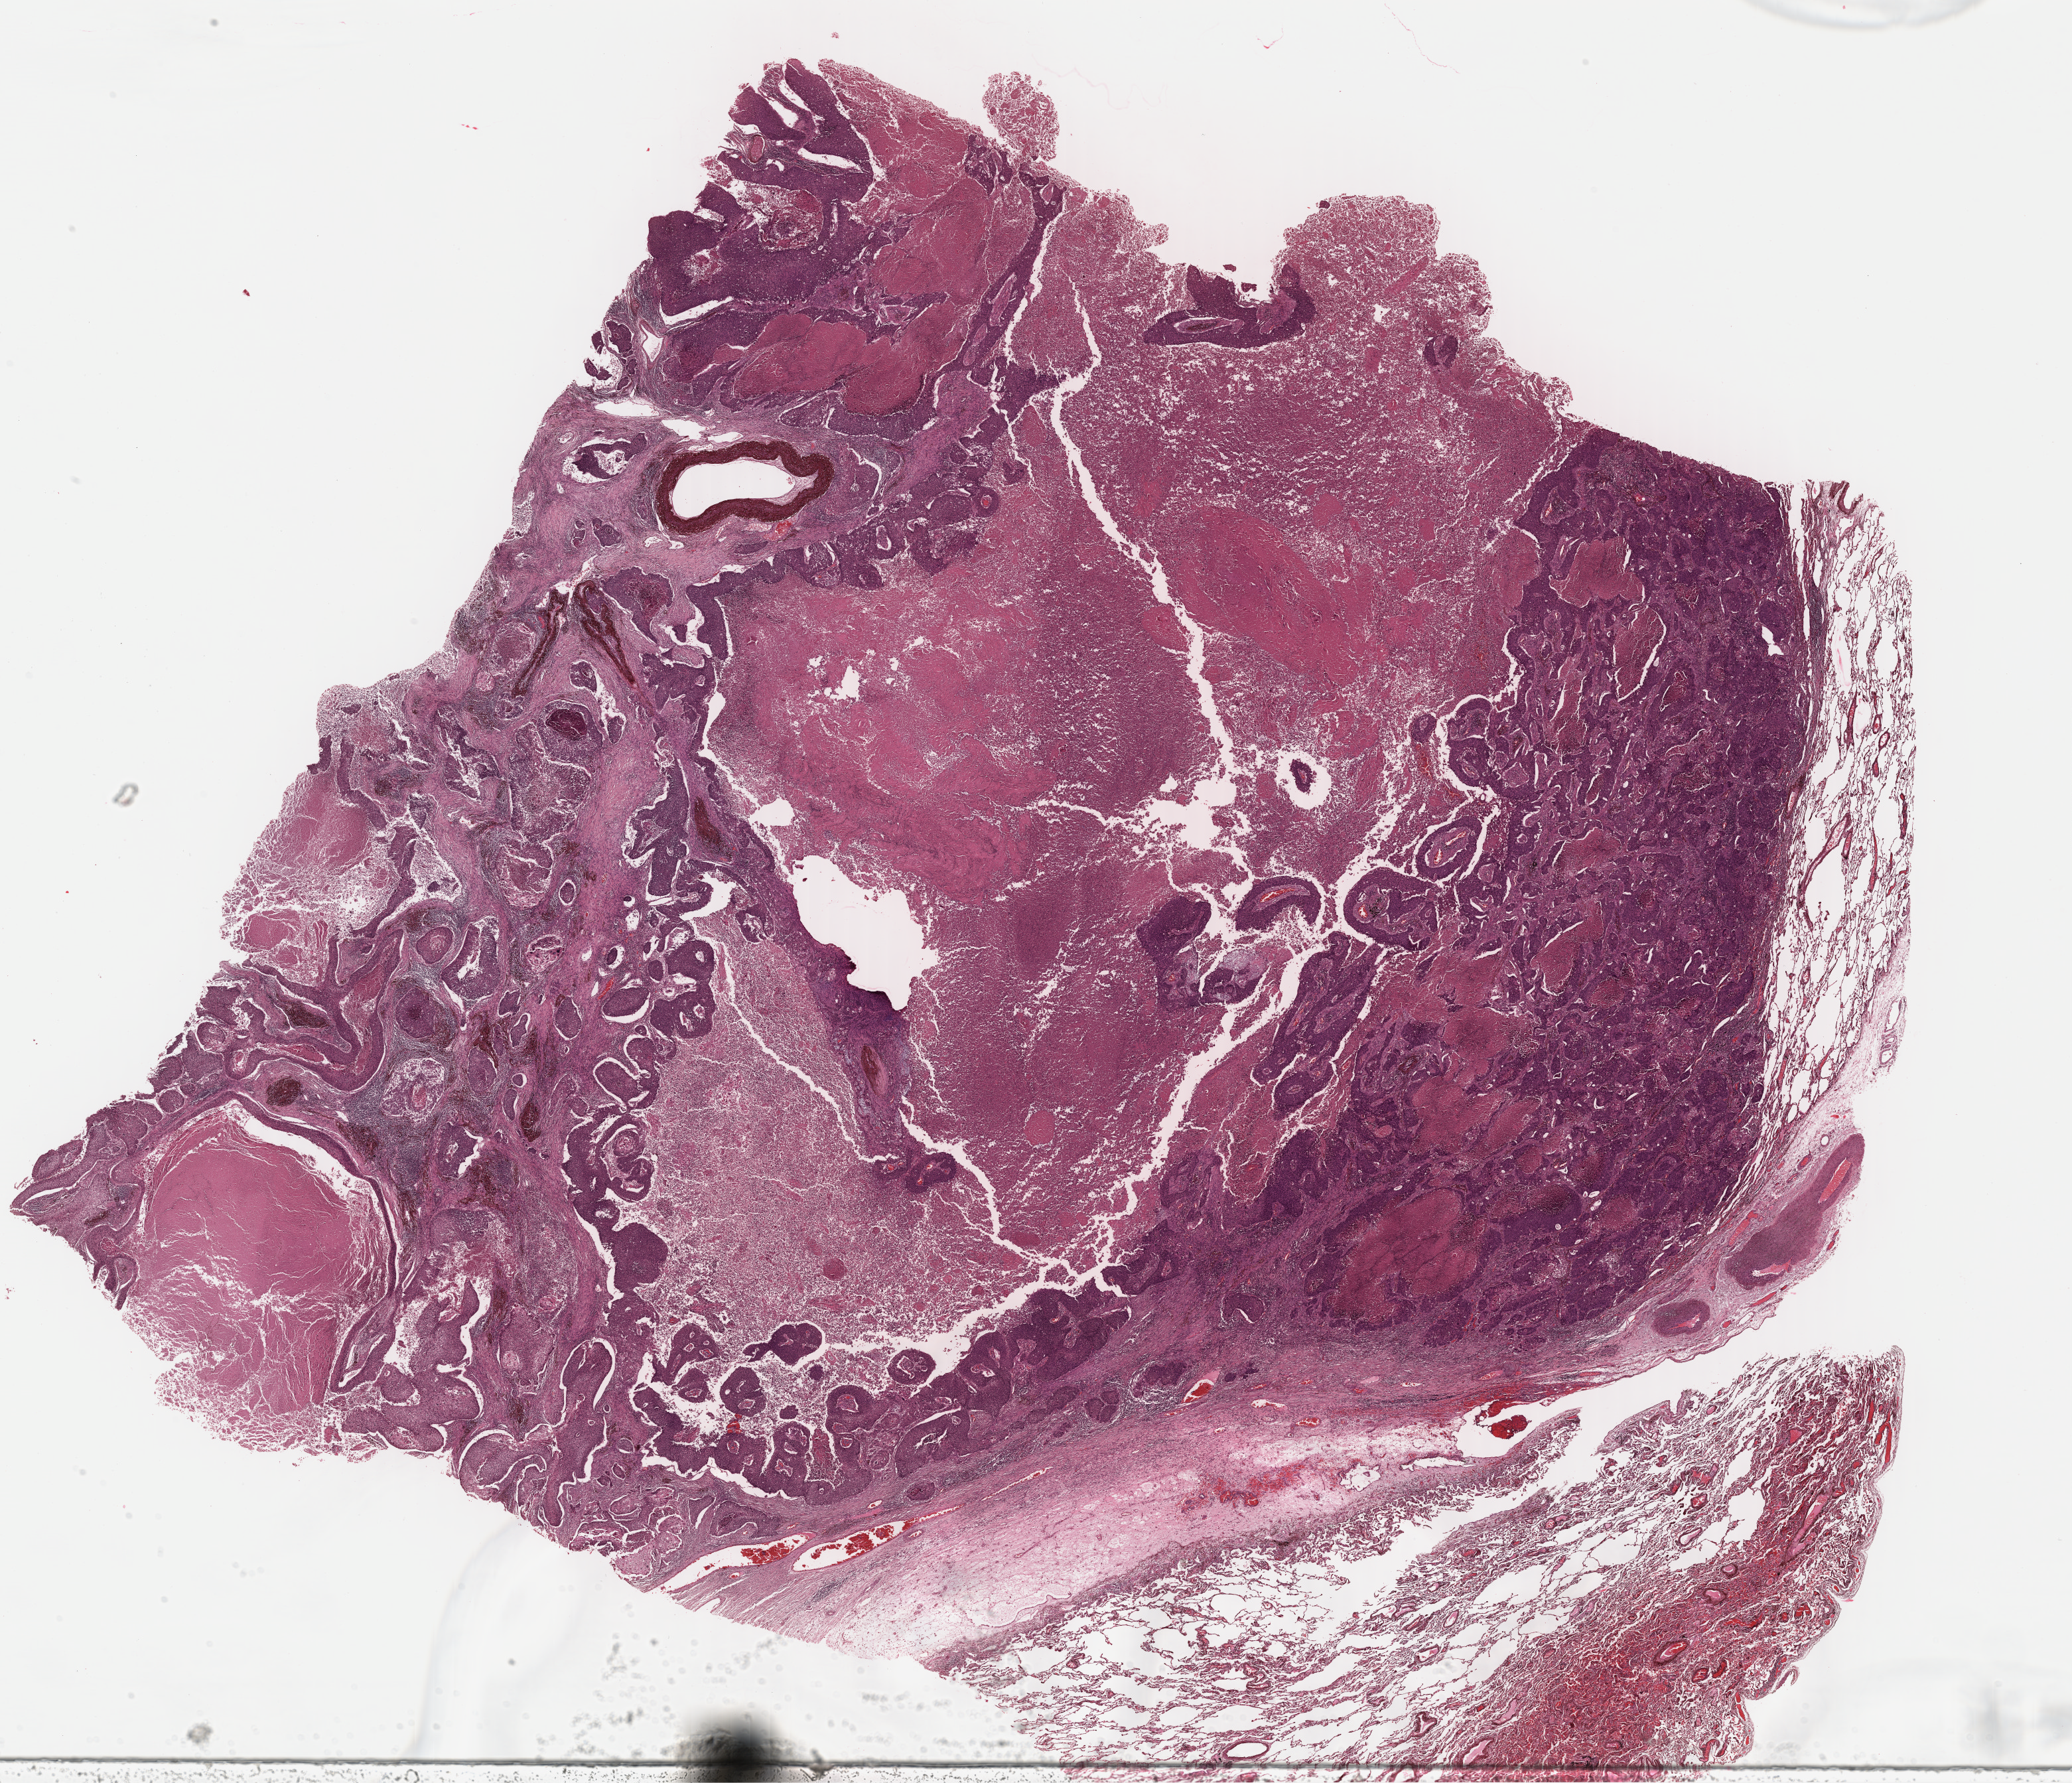
Whole-slide histology image, Hematoxylin and eosin (H&E) stained, a low-resolution overview of the entire scanned area, about 24.6 x 21.1 mm (from a 40x scan); formalin-fixed paraffin-embedded (FFPE) diagnostic section; lung, primary tumour sample. Patient: female, age at initial diagnosis 77 years.
AJCC pathologic stage: IB (6th edition). Laterality: right. Pathologic diagnosis: Squamous cell carcinoma, NOS (lower lobe, lung).